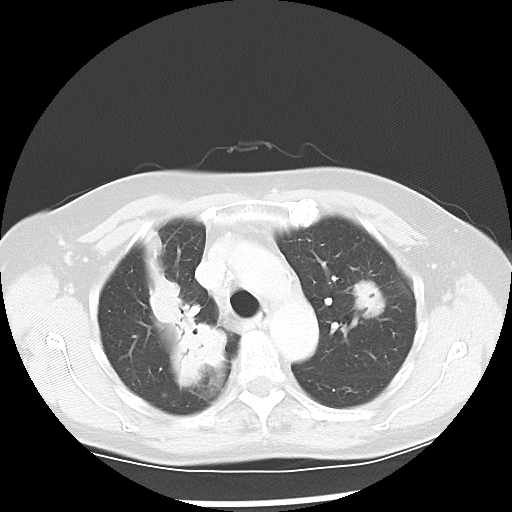
Chest CT, one axial slice. Slice 37 of 52 in the series (ordered by position). Lung window (W 1500 / L -600 HU). 512 × 512 image matrix, field of view 328 × 328 mm. Patient: female, 60 years. From the clinical record (not read from this slice): clinical TNM (as recorded): T2 N1 M1a.
Structures marked on this image (bounding box drawn by a radiologist):
- lung tumour (recorded histology: adenocarcinoma): bounding box [x1, y1, x2, y2] px = [143, 269, 229, 391]